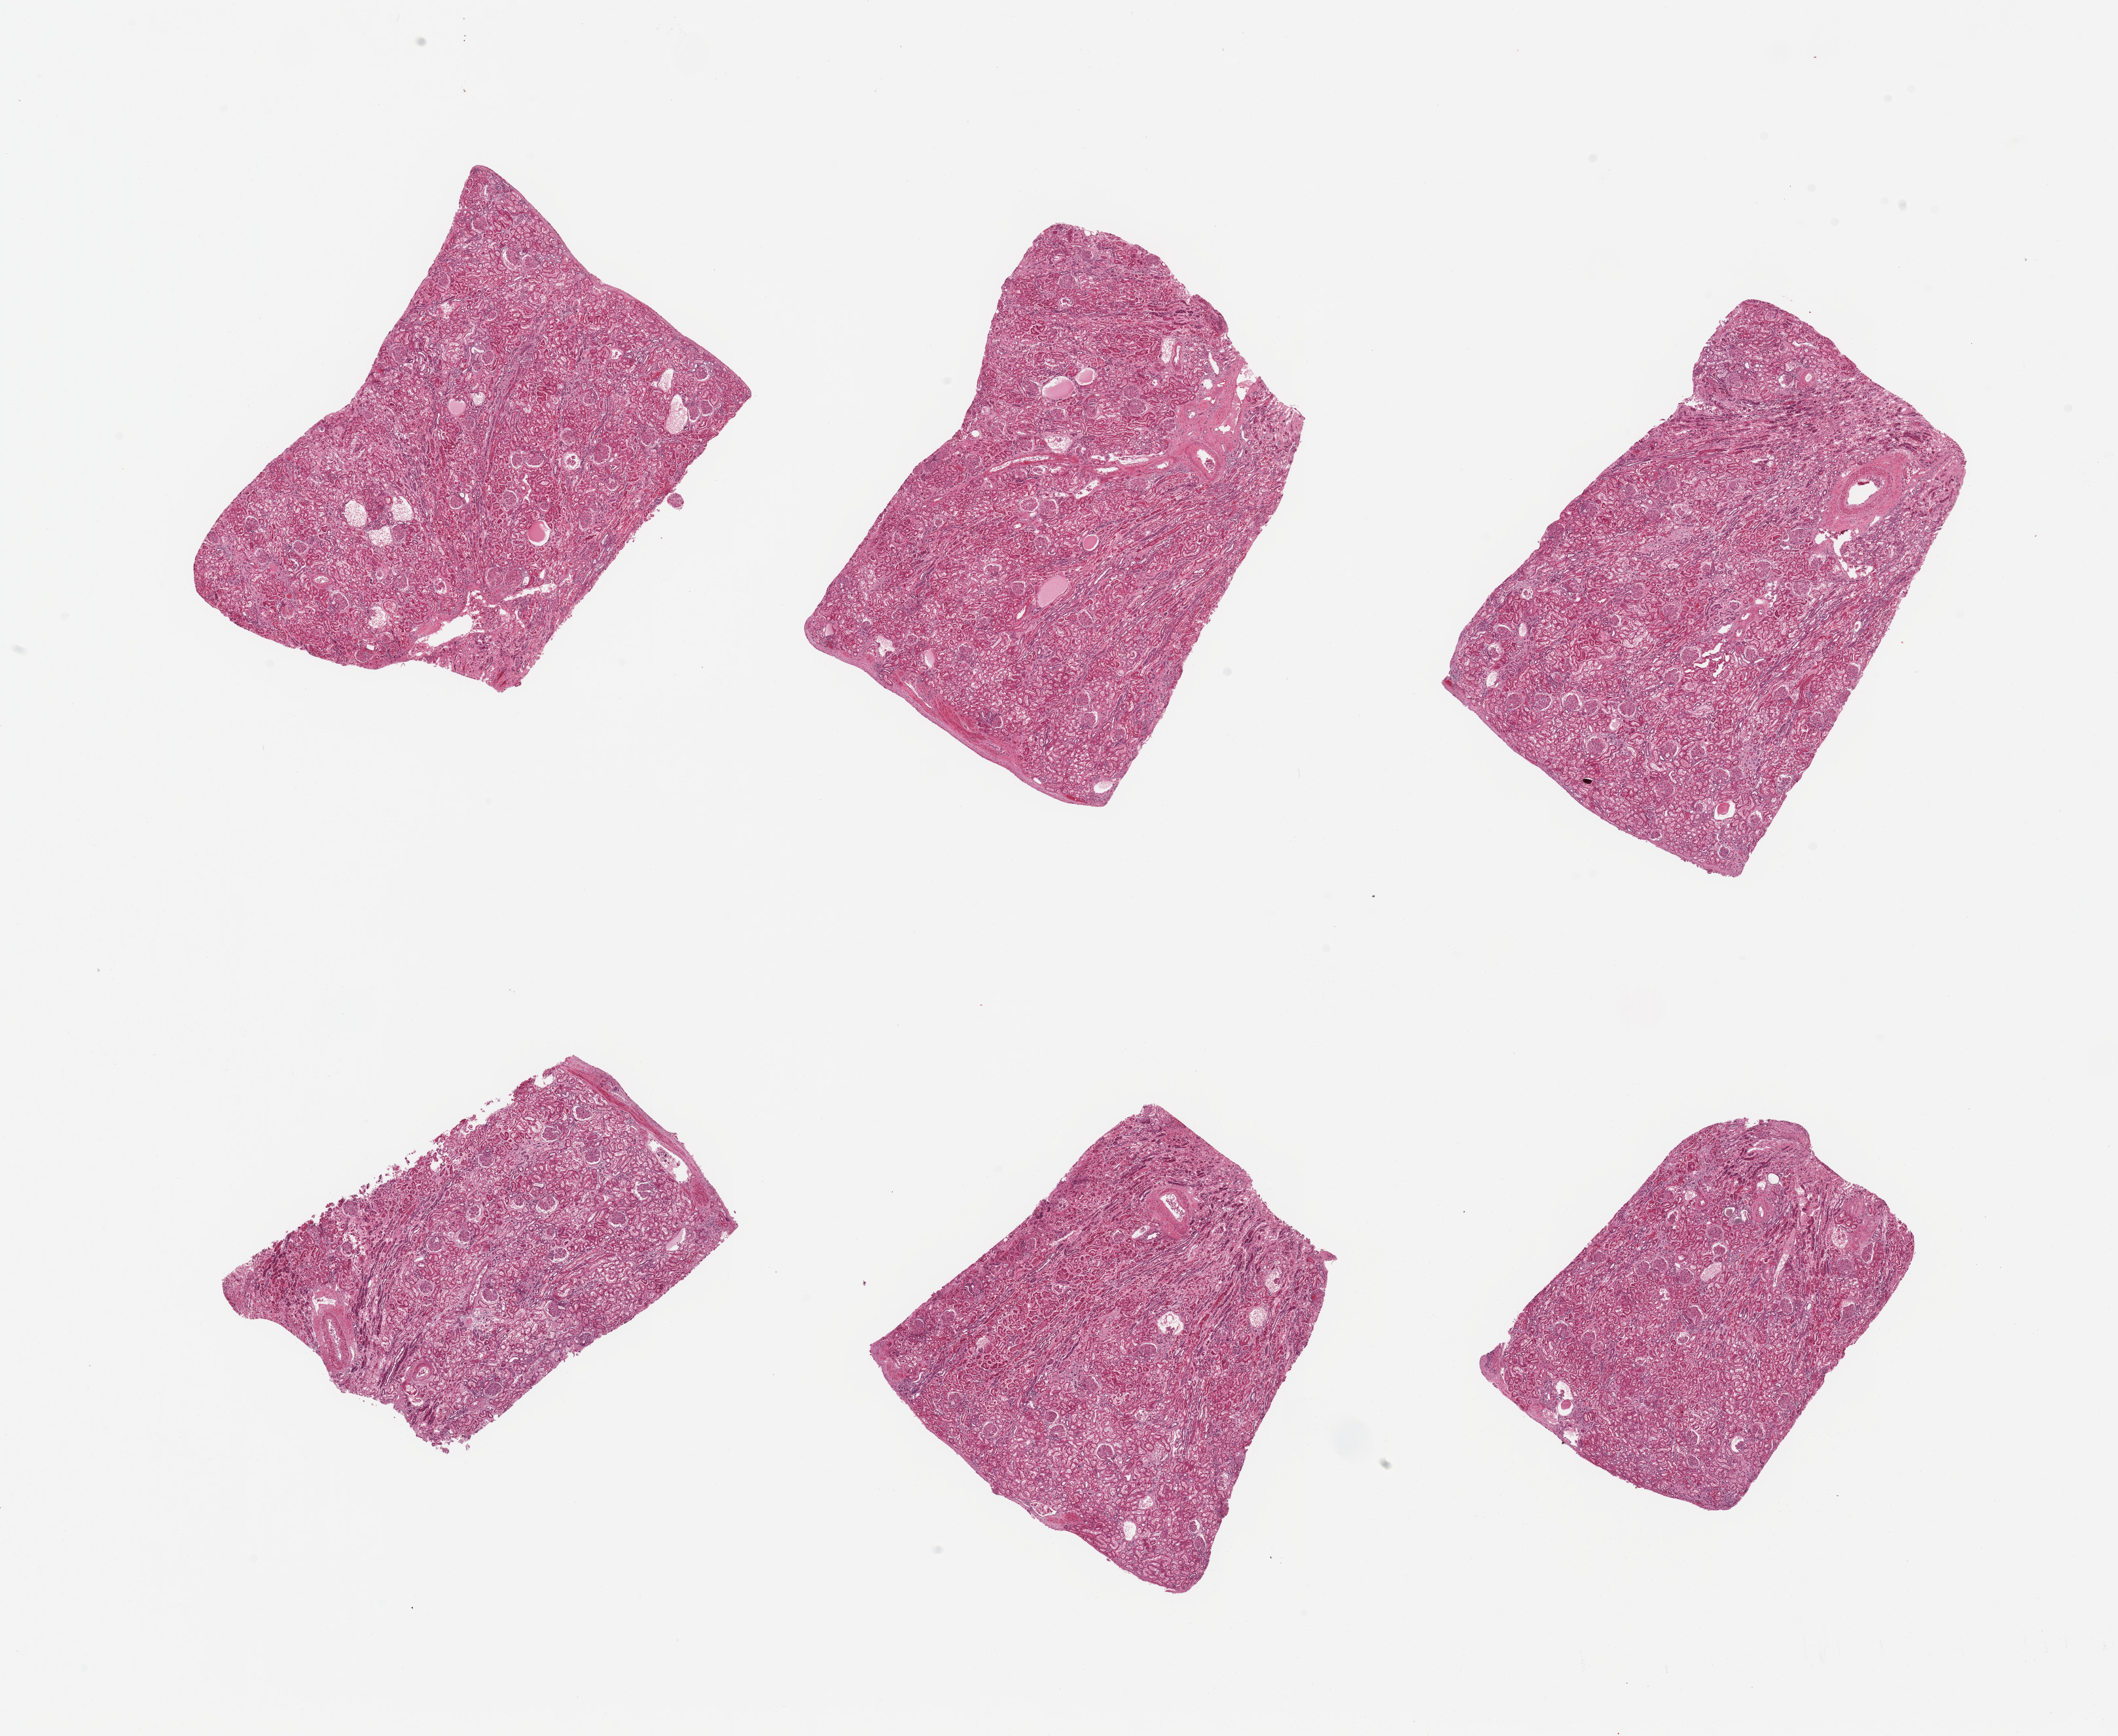
Digitized haematoxylin and eosin-stained section, brightfield — a low-resolution overview of the entire scanned area, about 25.6 x 21.0 mm; PAXgene-fixed paraffin-embedded (PFPE) section; section of renal cortex (target tissue); donor tissue sample. Donor: male.
Pathologist's review note for this sample: 6 pieces; glomeruli in better shape than tubules; no sign of chronic disease.